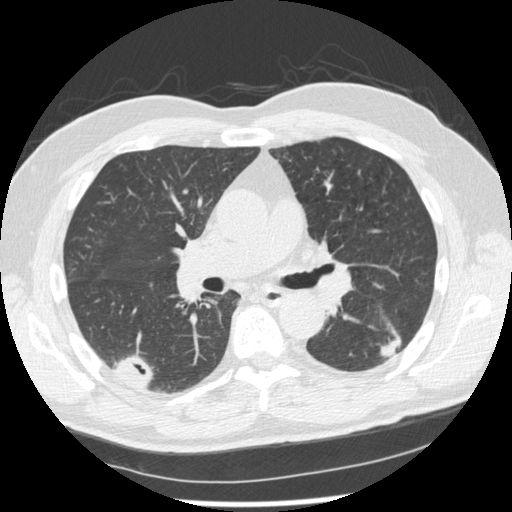
Chest CT (low-dose screening protocol), one axial image; second screening round (one year after baseline); lung window (W 1500 / L -600 HU); 512 × 512 image matrix, field of view 360 × 360 mm. Male participant, aged 74 years at enrolment.
Expert-annotated lung lesion, box from (x=372, y=317) to (x=420, y=369) px. The screening reader recorded 7 non-calcified nodules or masses ≥4 mm on this exam (right upper lobe, right lower lobe, right upper lobe, right lower lobe, left lower lobe, left upper lobe, left upper lobe); which of them this box marks is not recorded. Lung cancer was diagnosed 43 days after this screen: squamous cell carcinoma, NOS, left lower lobe, well differentiated (G1), stage IA (AJCC 6th edition), 28 mm at pathology.